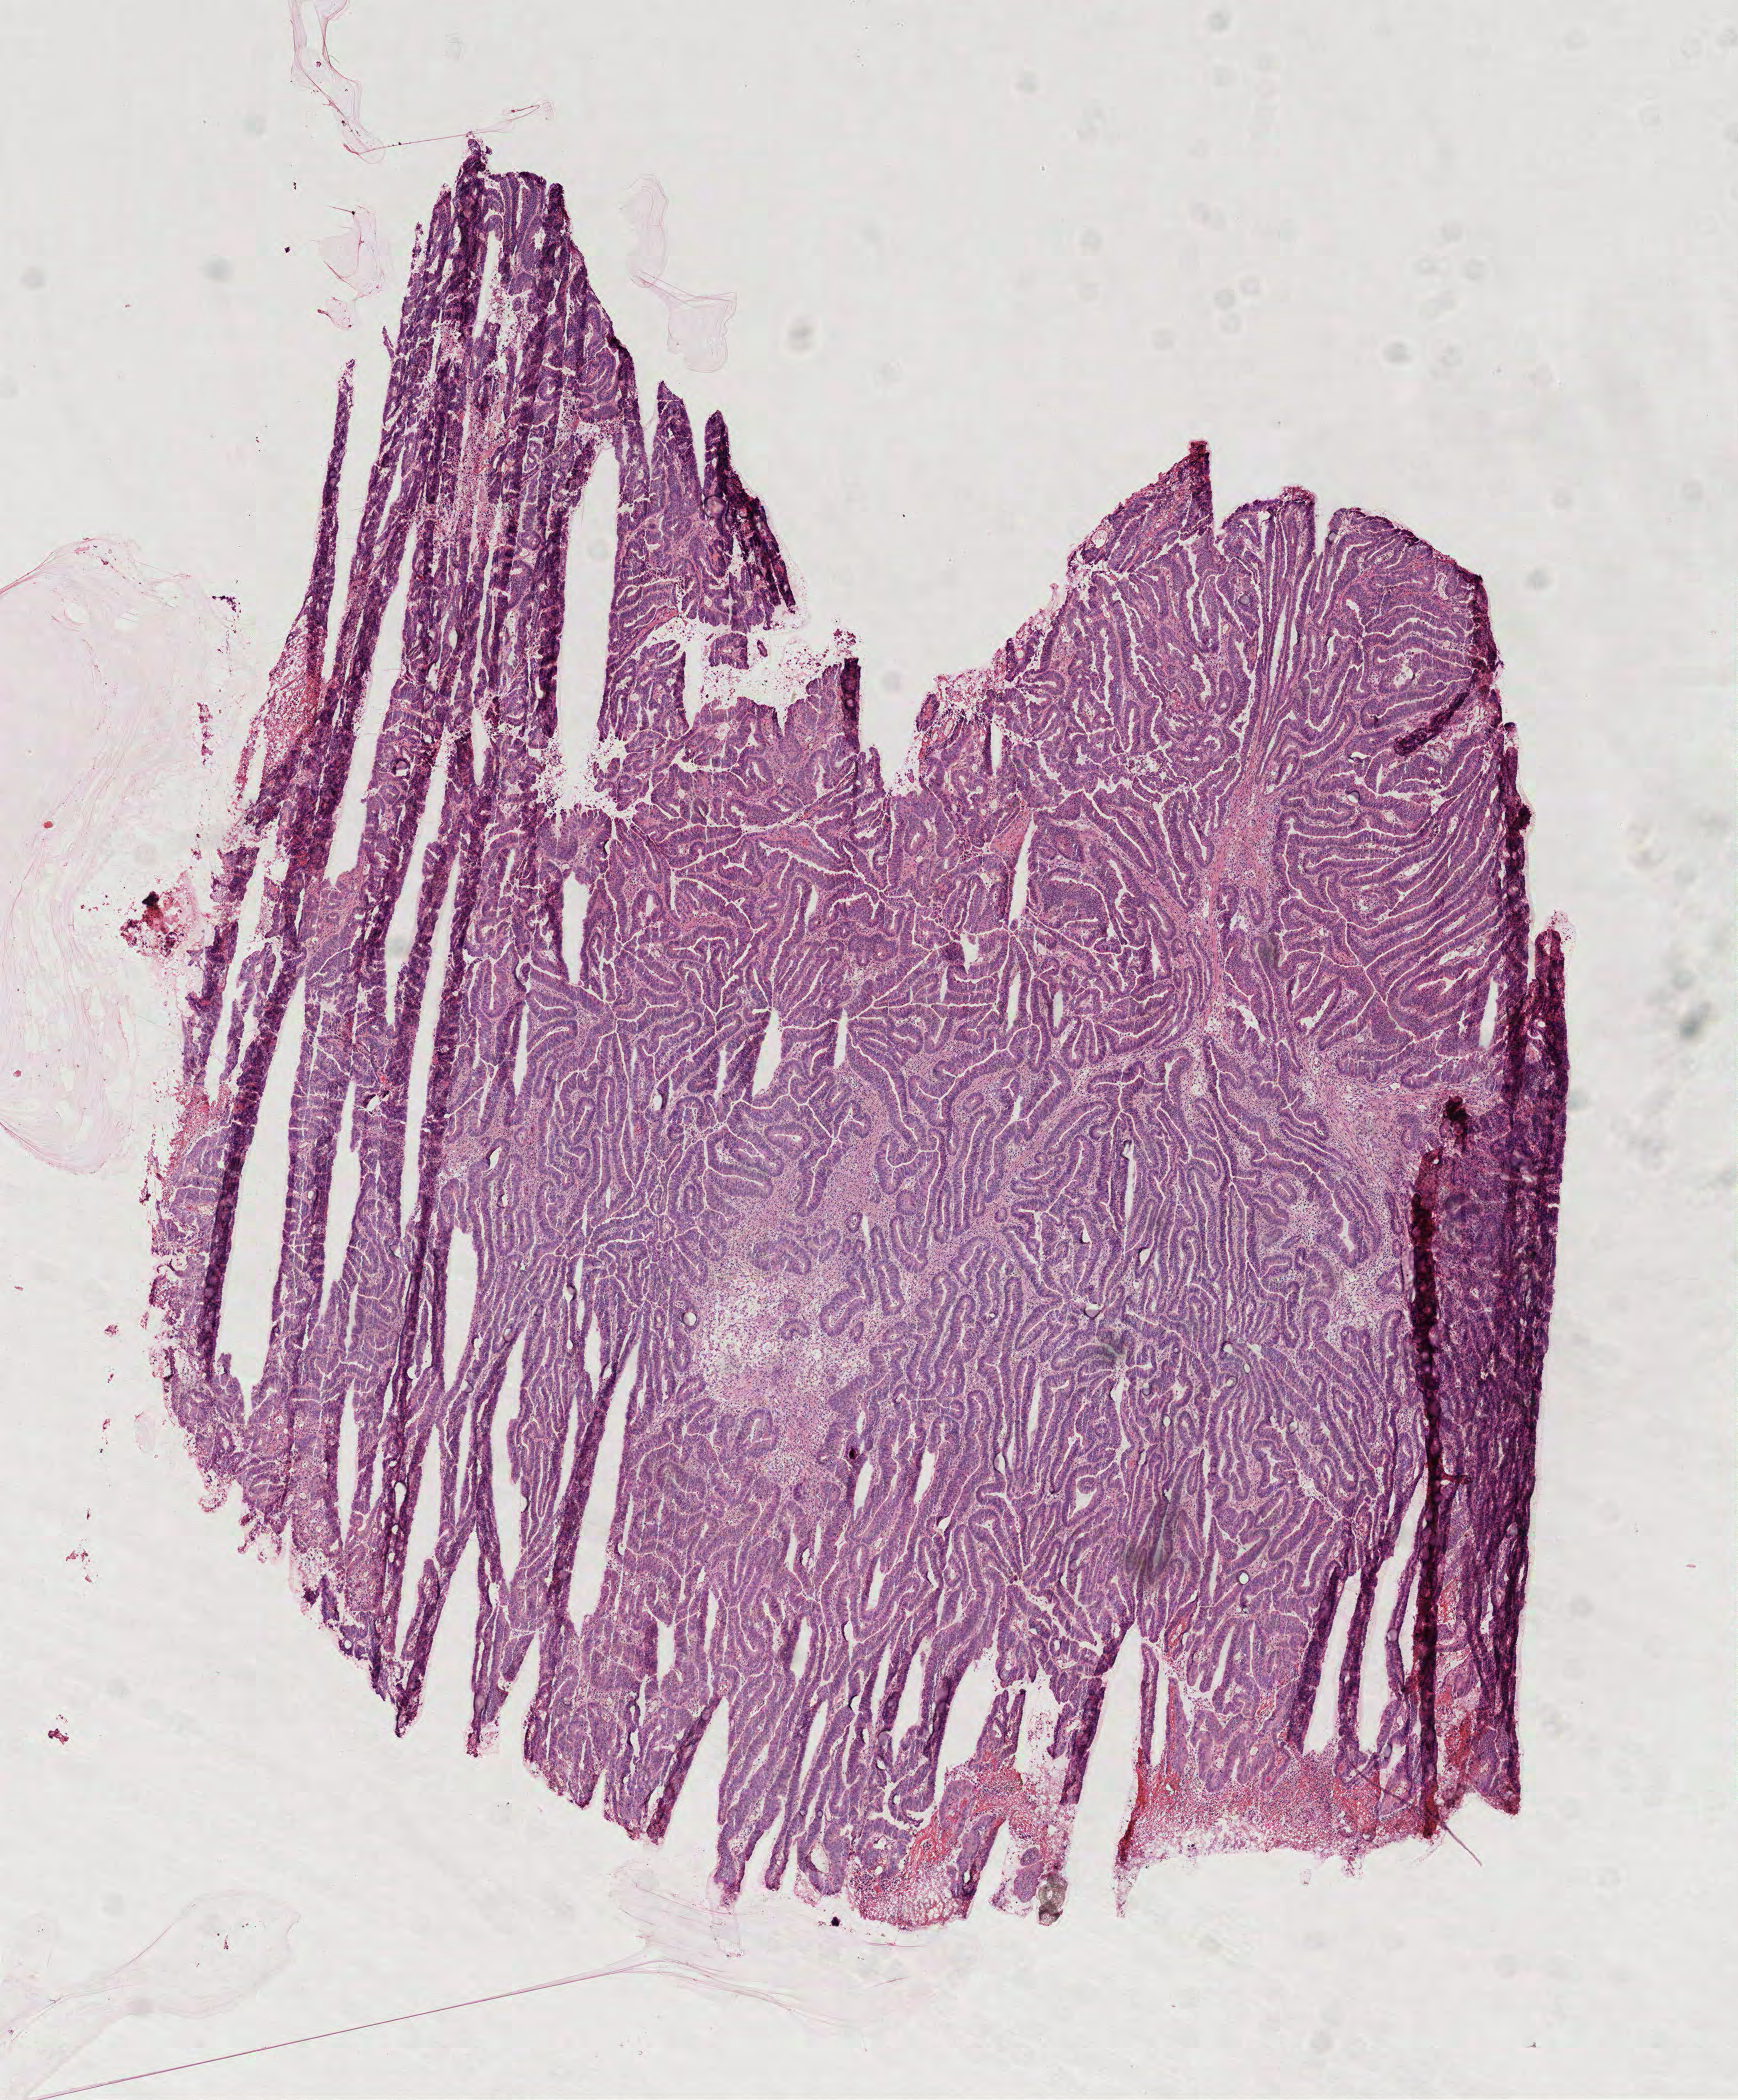
Digitized Hematoxylin and eosin (H&E) stained tissue section (whole slide) — a low-resolution overview of the entire scanned area, about 7.0 x 8.5 mm (slide scanned at 40x); frozen section from the top of the tissue portion; colon, primary tumour sample. Patient: male, age at initial diagnosis 64 years.
Histologic diagnosis: Adenocarcinoma, NOS (transverse colon).